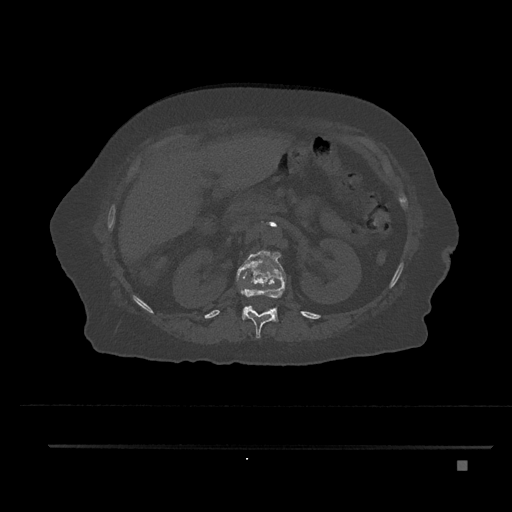
CT including the spine, one axial slice. Position 242 of 797 along the scan axis. Reconstruction kernel Br40s/3. Bone window (W 1800 / L 400 HU). 0.5 mm slice thickness. 512 × 512 image matrix, field of view 437 × 437 mm. Female patient, age 76 years. From the clinical record (not read from this slice): primary cancer: lung; vertebrae with lytic lesions (as recorded): T11, L3.
Outlined on this slice (semi-automatic segmentation, software-assisted and operator-edited):
- L1 vertebra: bounding box [x1, y1, x2, y2] px = [236, 250, 286, 322]
- T12 vertebra: [239, 283, 274, 339]